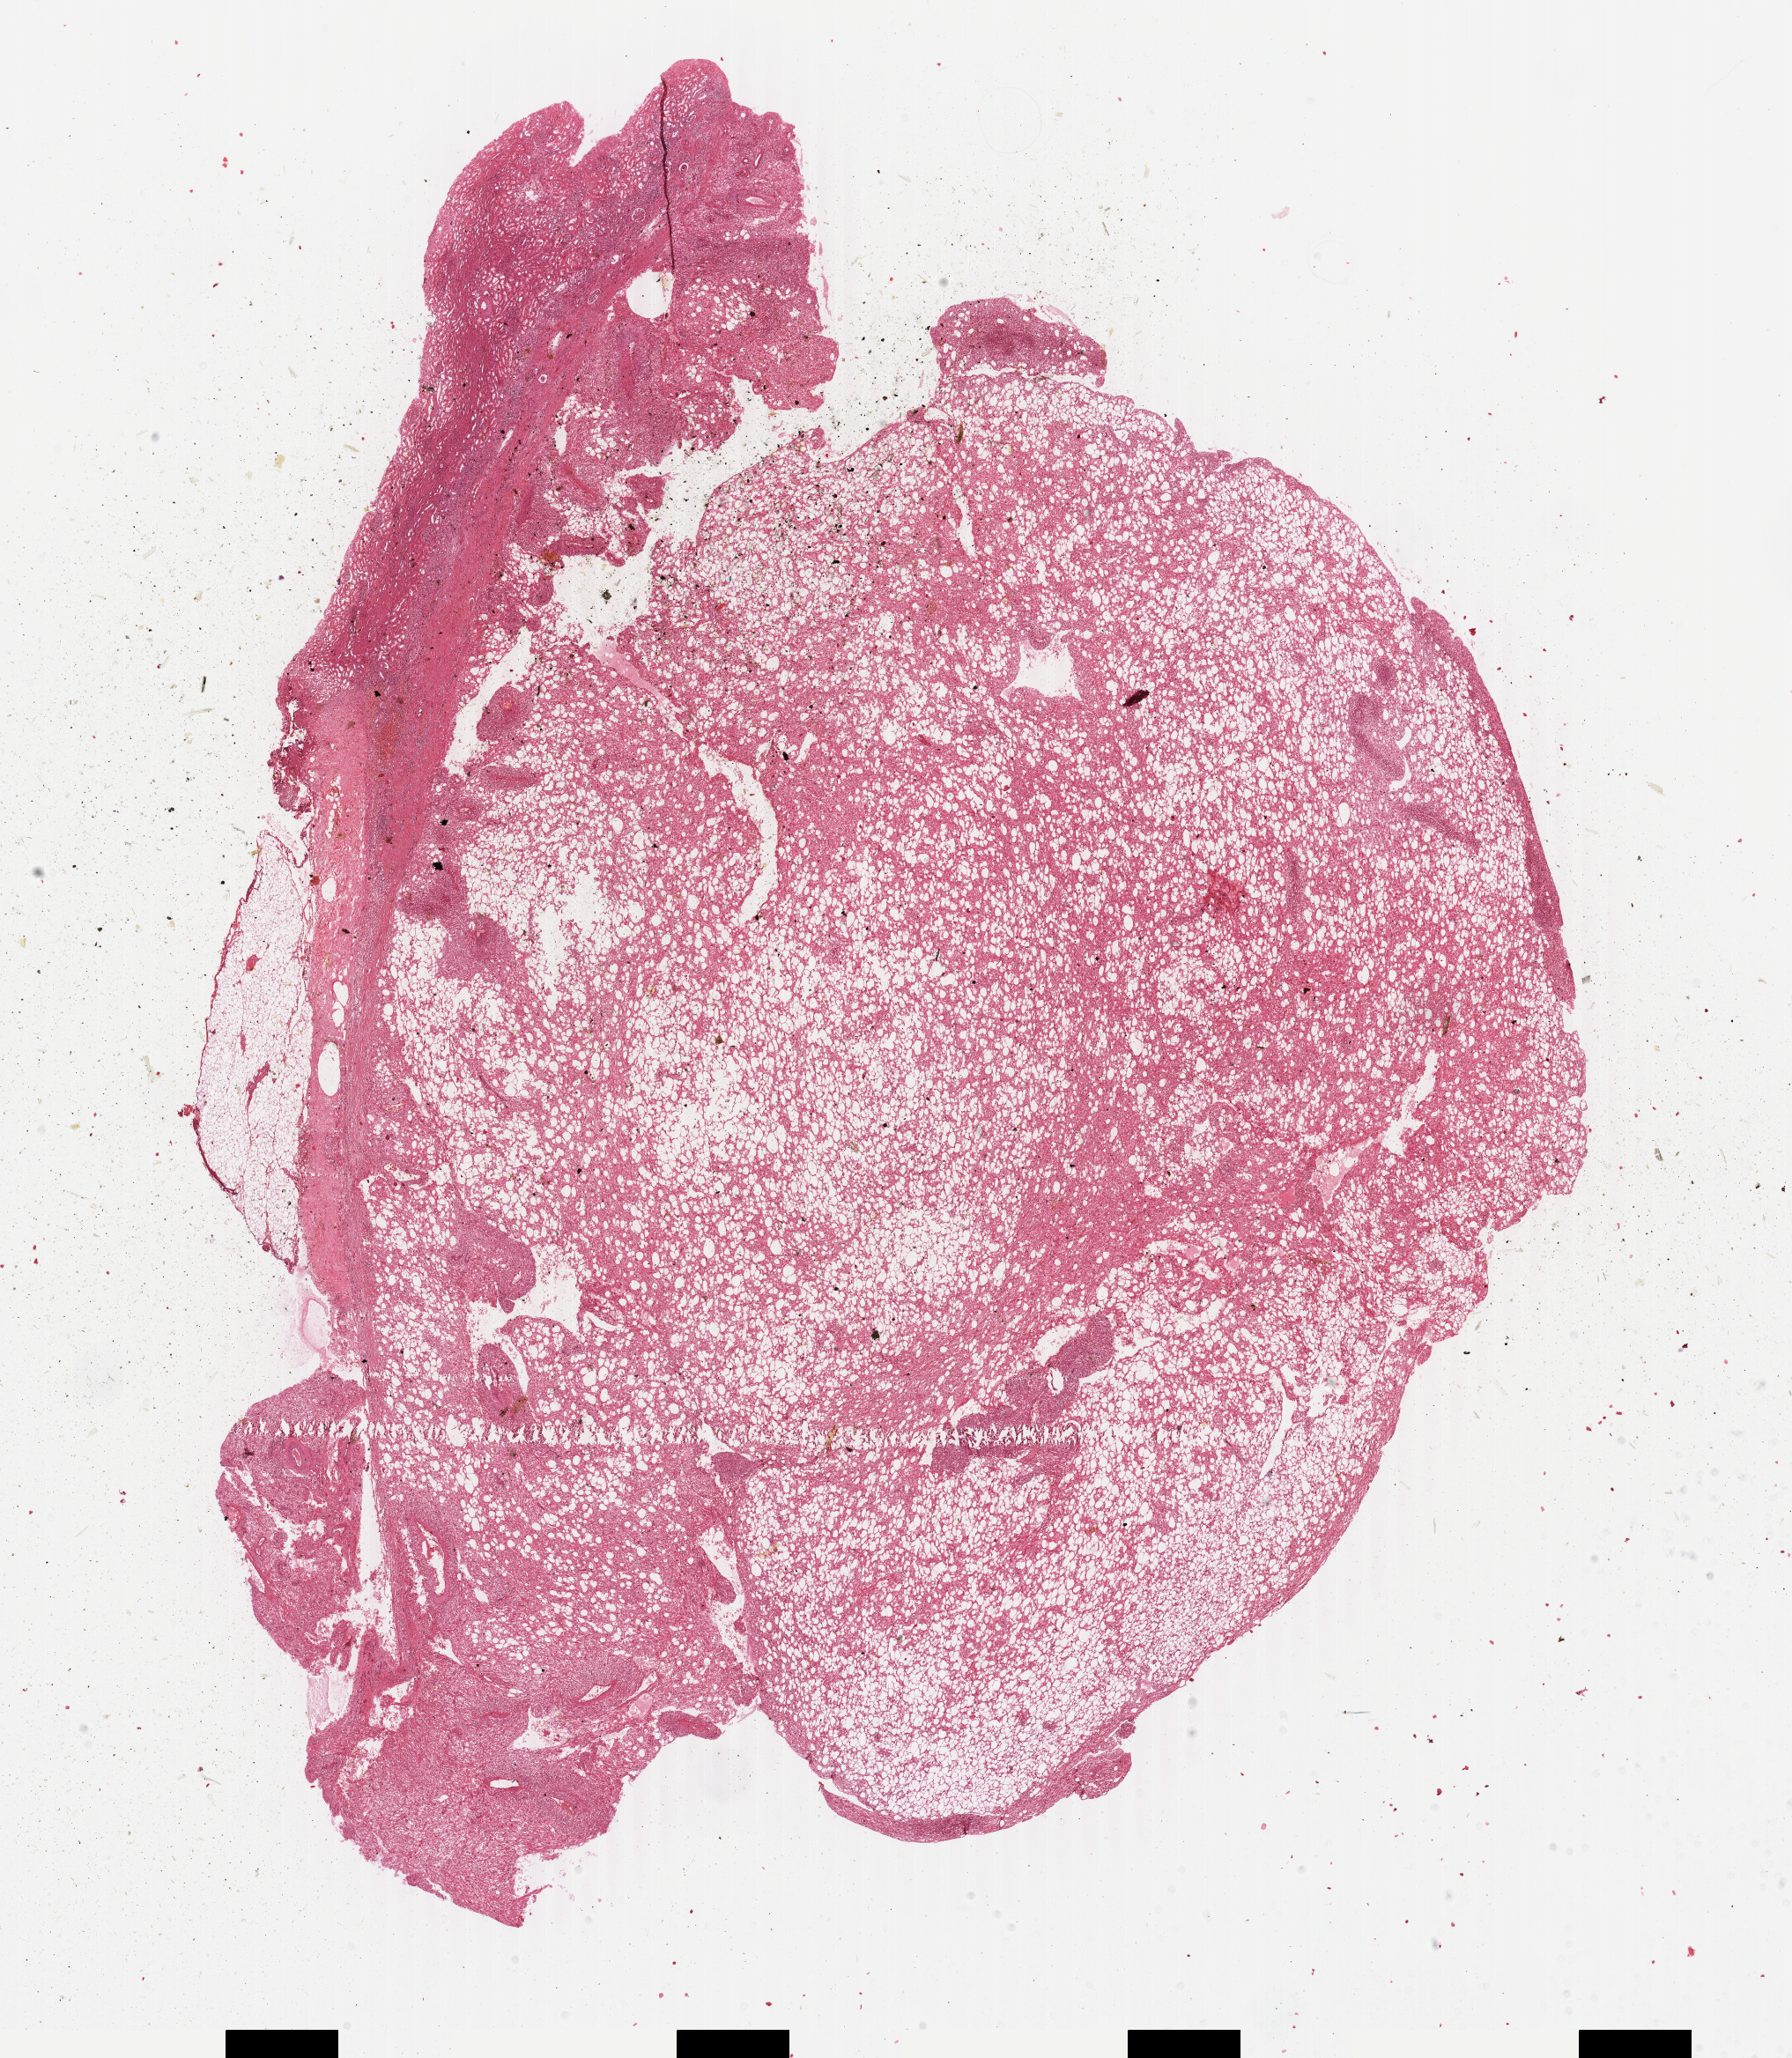
Whole-slide histology image, H&E, shown as a low-resolution overview of the whole scanned area (about 16.2 x 18.6 mm). Formalin-fixed paraffin-embedded (FFPE) diagnostic section. Primary tumour sample from the retroperitoneum and peritoneum. Female patient; age at initial diagnosis 37 years.
Histologic diagnosis: Liposarcoma, well differentiated (retroperitoneum).